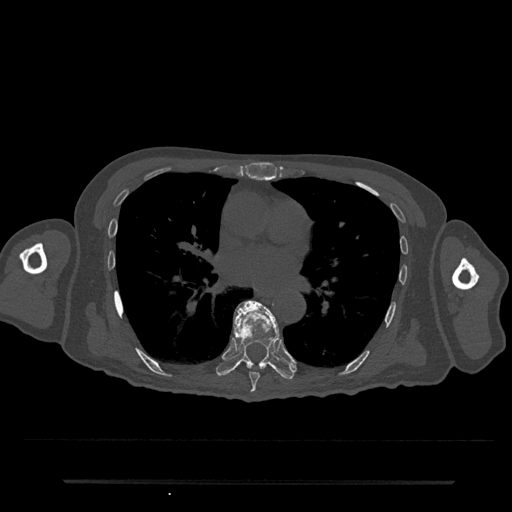
CT including the spine, one axial slice. Position 445 of 797 along the scan axis. 120 kVp. Bone window (W 1800 / L 400 HU). 0.5 mm slice thickness. 512 × 512 image matrix. Patient: male, 74 years. Case-level facts recorded for this patient, not image findings: primary cancer: prostate.
Annotated regions visible in this slice (semi-automatic segmentation, software-assisted and operator-edited):
- T7 vertebra: bounding box (x1, y1, x2, y2) in pixels: (249, 302, 266, 393)
- T8 vertebra: (216, 300, 295, 380)